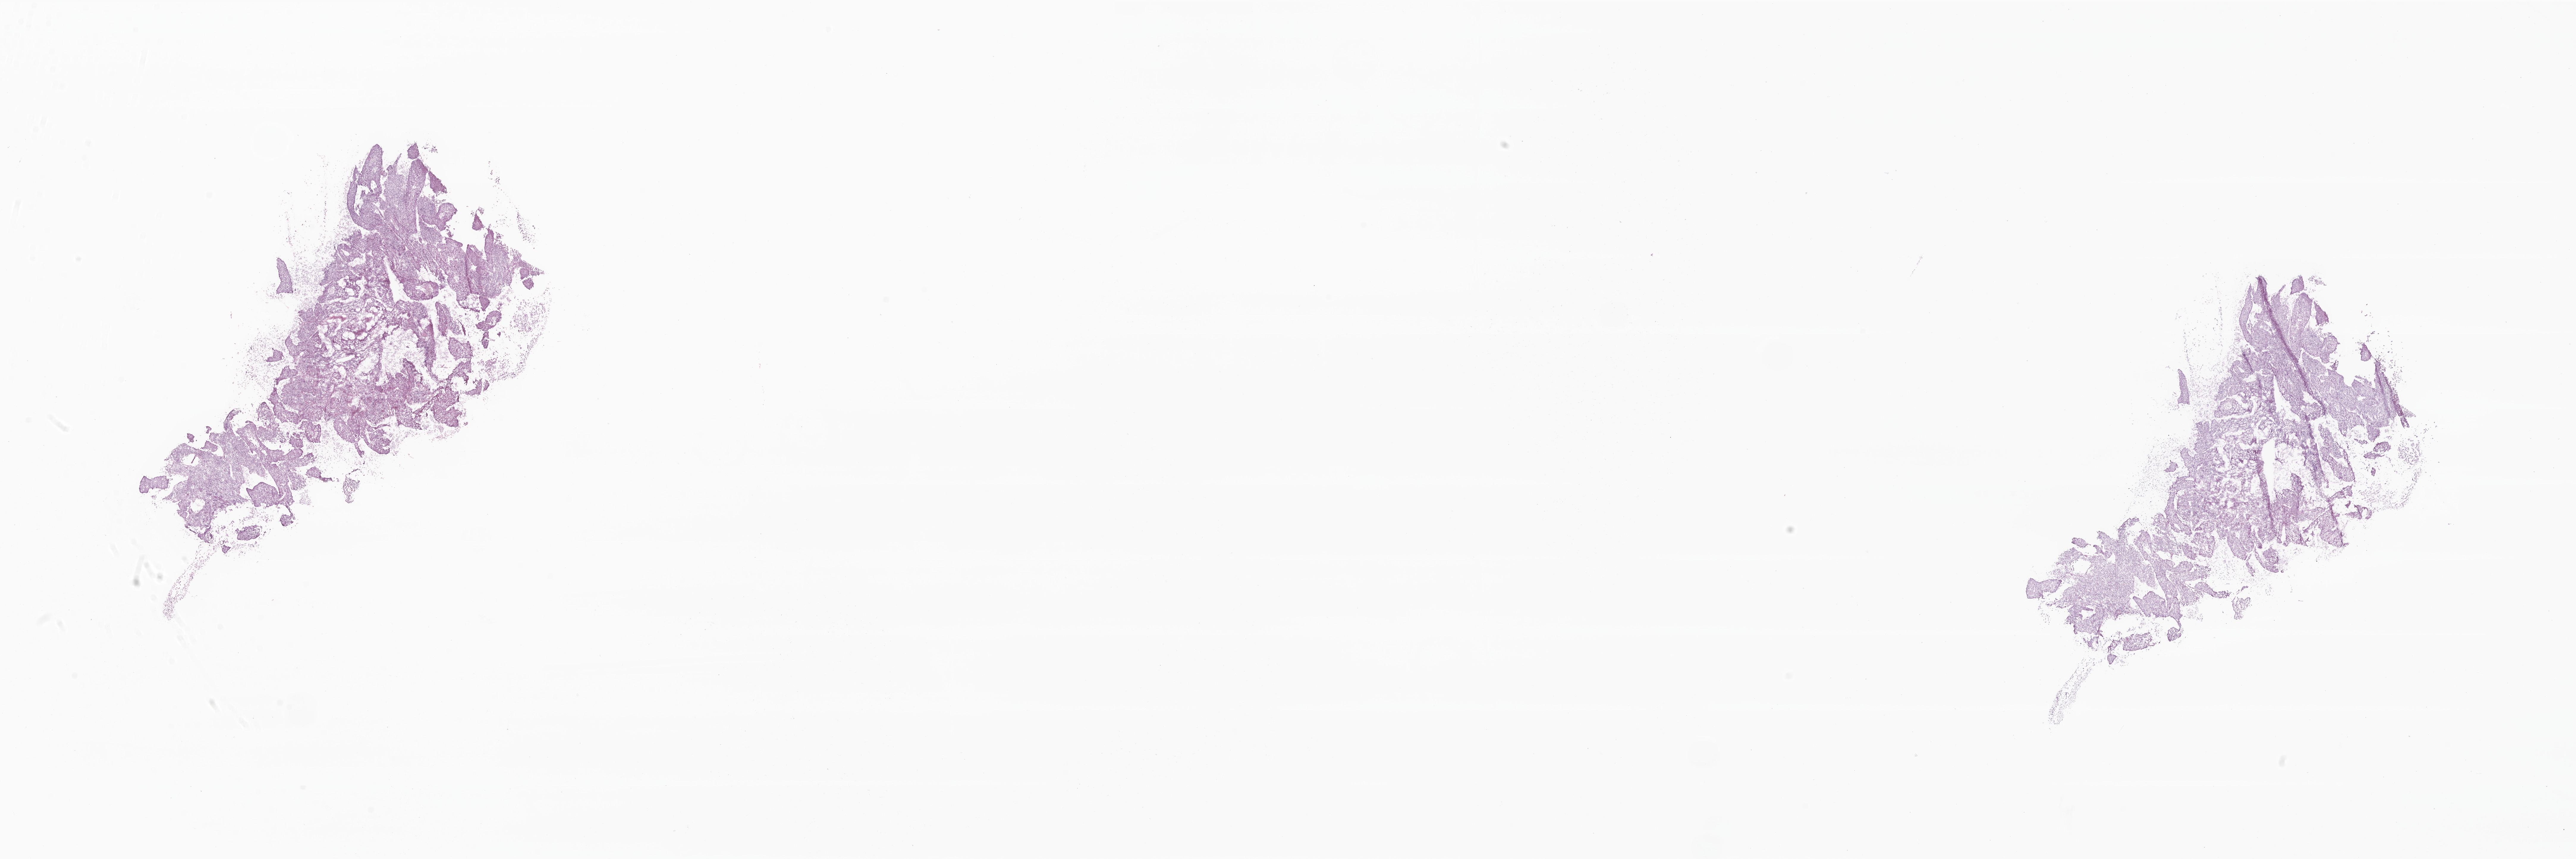
H&E whole-slide image of tumor tissue from the lateral wall of nasopharynx — shown as a low-resolution overview of the whole scanned area (about 36.5 x 12.2 mm). Frozen section (OCT-embedded). Male patient, age 201 months (16 years 9 months).
Diagnosis: Carcinoma, metastatic, NOS.